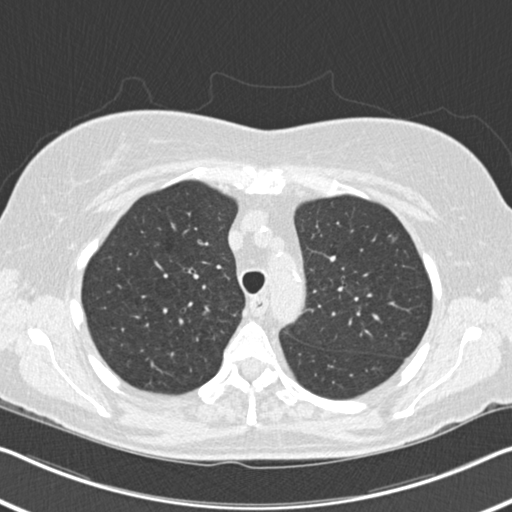
Chest CT (low-dose screening protocol), one axial image; second annual screen; lung window (W 1500 / L -600 HU); 2 mm slice thickness. Female participant, aged 60 years at enrolment.
• Expert-annotated lung lesion, bounding box <377,226,415,264> (left, top, right, bottom; pixels).
• The screening reader recorded 6 non-calcified nodules or masses ≥4 mm on this exam (right upper lobe, right middle lobe, right lower lobe, right lower lobe, left lower lobe, lingula); which of them this box marks is not recorded.
• Later outcome: lung cancer diagnosed 495 days after this screen (after the third annual screen) — non-small cell carcinoma, left upper lobe, poorly differentiated (G3), stage IB (AJCC 6th edition), 7 mm at pathology.